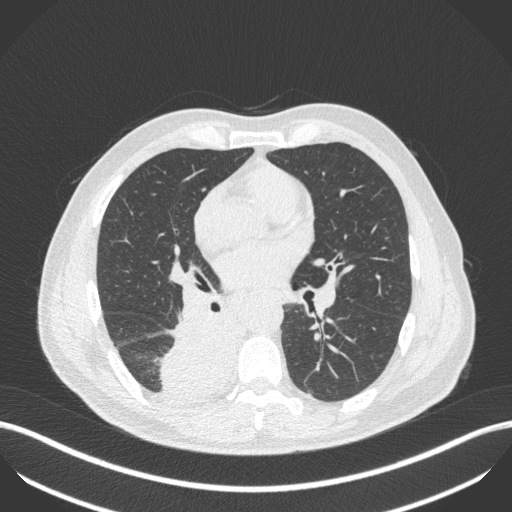
Chest CT, one axial slice; position 245 of 451 along the scan axis; reconstruction kernel B31f; 100 kVp; lung window (W 1500 / L -600 HU); 1 mm slice thickness; 512 × 512 image matrix, field of view 400 × 400 mm. Male patient, age 61 years. From the clinical record (not read from this slice): clinical TNM (as recorded): T1 N0 M0; histopathological grade: G3.
Outlined on this slice (rectangle marked by the reading radiologist):
- lung tumour (recorded histology: small cell carcinoma): bounding box [x1, y1, x2, y2] px = [152, 310, 246, 413]